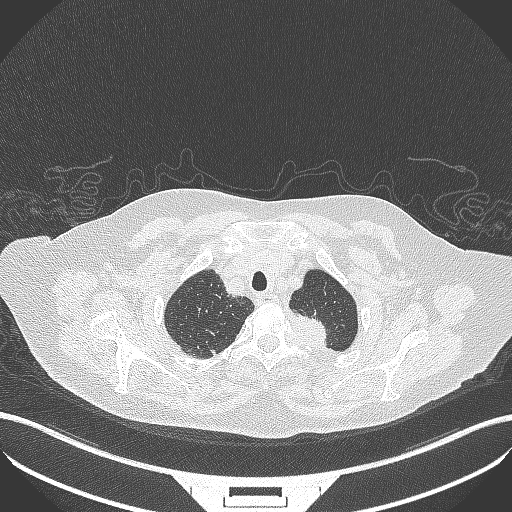
Chest CT, one axial slice. Position 304 of 353 along the scan axis. Reconstruction kernel B70f. 100 kVp. Lung window (W 1500 / L -600 HU). 1 mm slice thickness. 512 × 512 image matrix, field of view 400 × 400 mm. Female patient, age 81 years. From the clinical record (not read from this slice): clinical TNM (as recorded): T2a N0 M0.
Annotated regions visible in this slice (rectangle marked by the reading radiologist):
- lung tumour (recorded histology: adenocarcinoma): bounding box (x1, y1, x2, y2) in pixels: (283, 306, 331, 348)